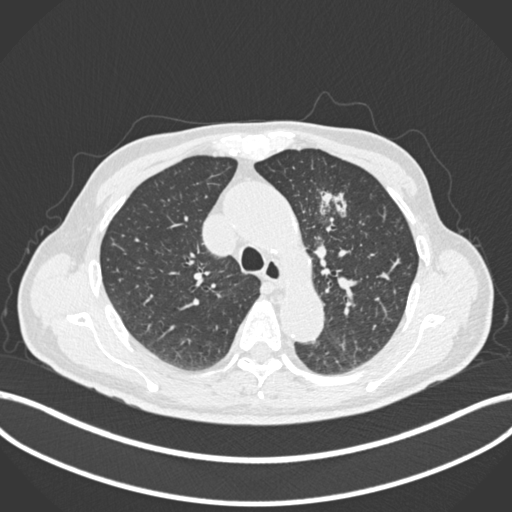
Chest CT, one axial slice; position 176 of 261 along the scan axis; 120 kVp; lung window (W 1500 / L -600 HU); 512 × 512 image matrix, field of view 400 × 400 mm. Patient: male, 74 years. From the clinical record (not read from this slice): clinical TNM (as recorded): T2b N0 M1c.
Annotated regions visible in this slice (bounding box drawn by a radiologist):
- lung tumour (recorded histology: adenocarcinoma): bounding box (x1, y1, x2, y2) in pixels: (316, 190, 351, 220)